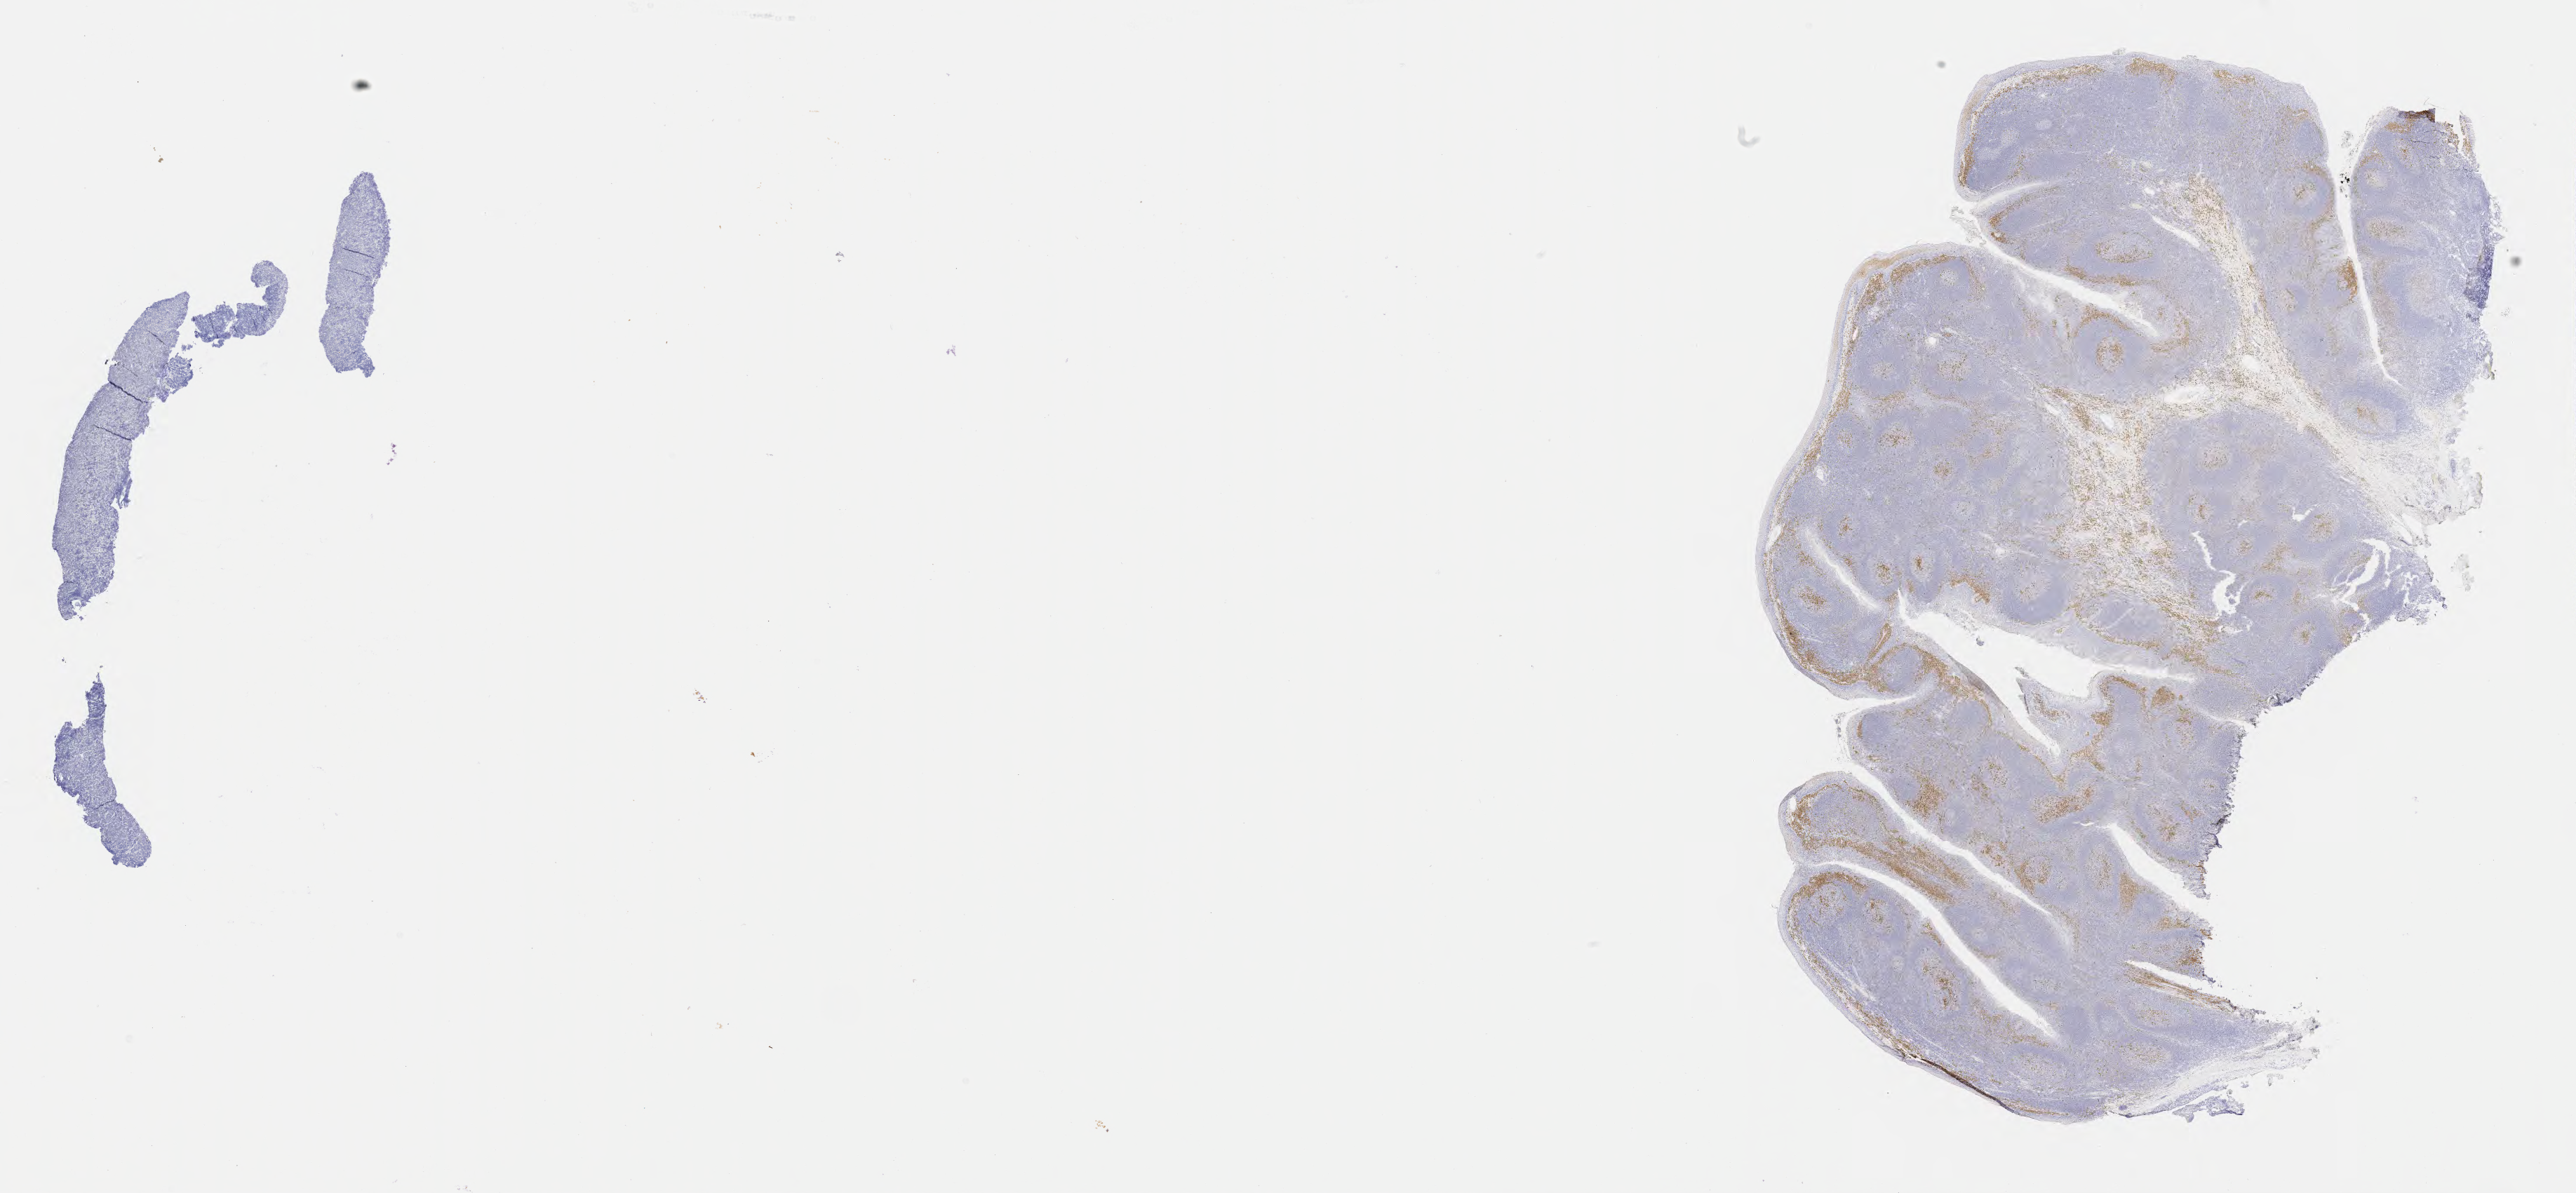
Whole-slide image, immunohistochemical stain for IRF4/MUM1, shown as a low-resolution overview of the whole scanned area (about 29.7 x 13.8 mm). Specimen: tumor tissue. Patient male; age 10 years.
Diagnosis: Diffuse large B-cell lymphoma, NOS.